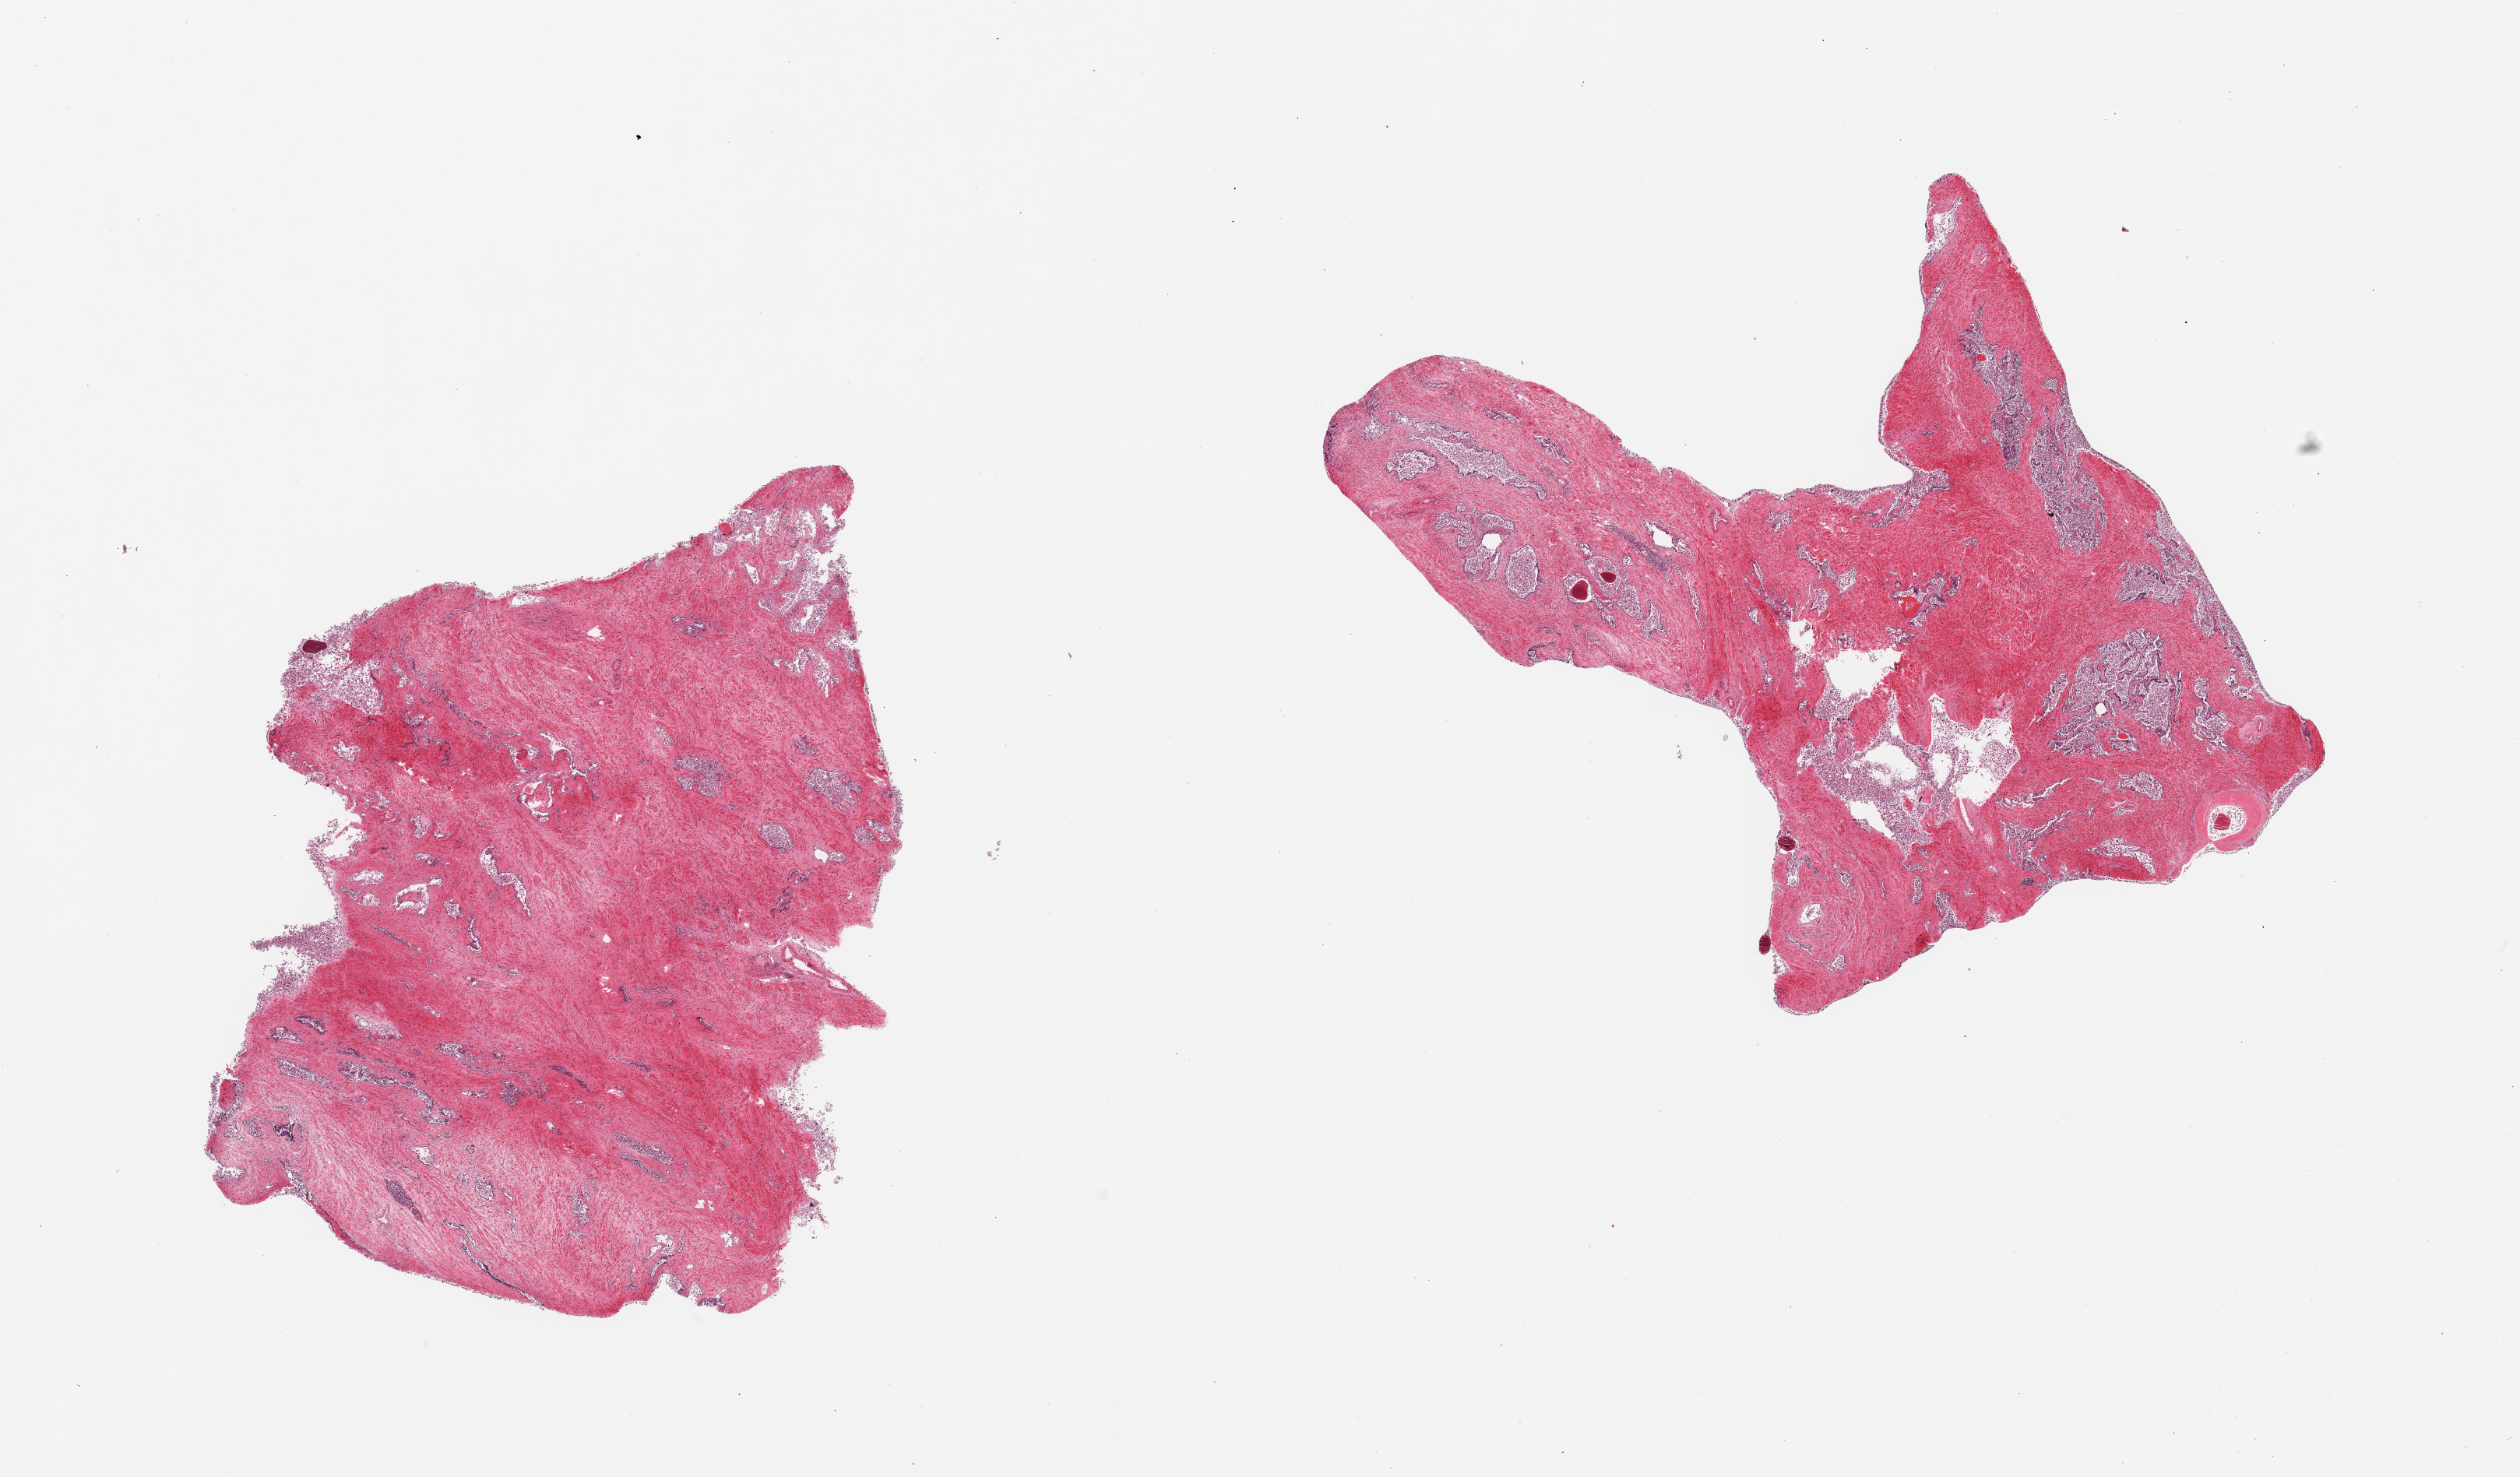
Whole-slide image, hematoxylin and eosin (H&E) stain — whole scanned area (about 25.6 x 15.0 mm) shown as a low-resolution overview. PAXgene-fixed paraffin-embedded (PFPE) section. Target tissue: prostate. Tissue donor sample. Donor sex: male.
* pathologist's review note for this sample: 2 pieces; glands totally autolyzed, stroma preserved